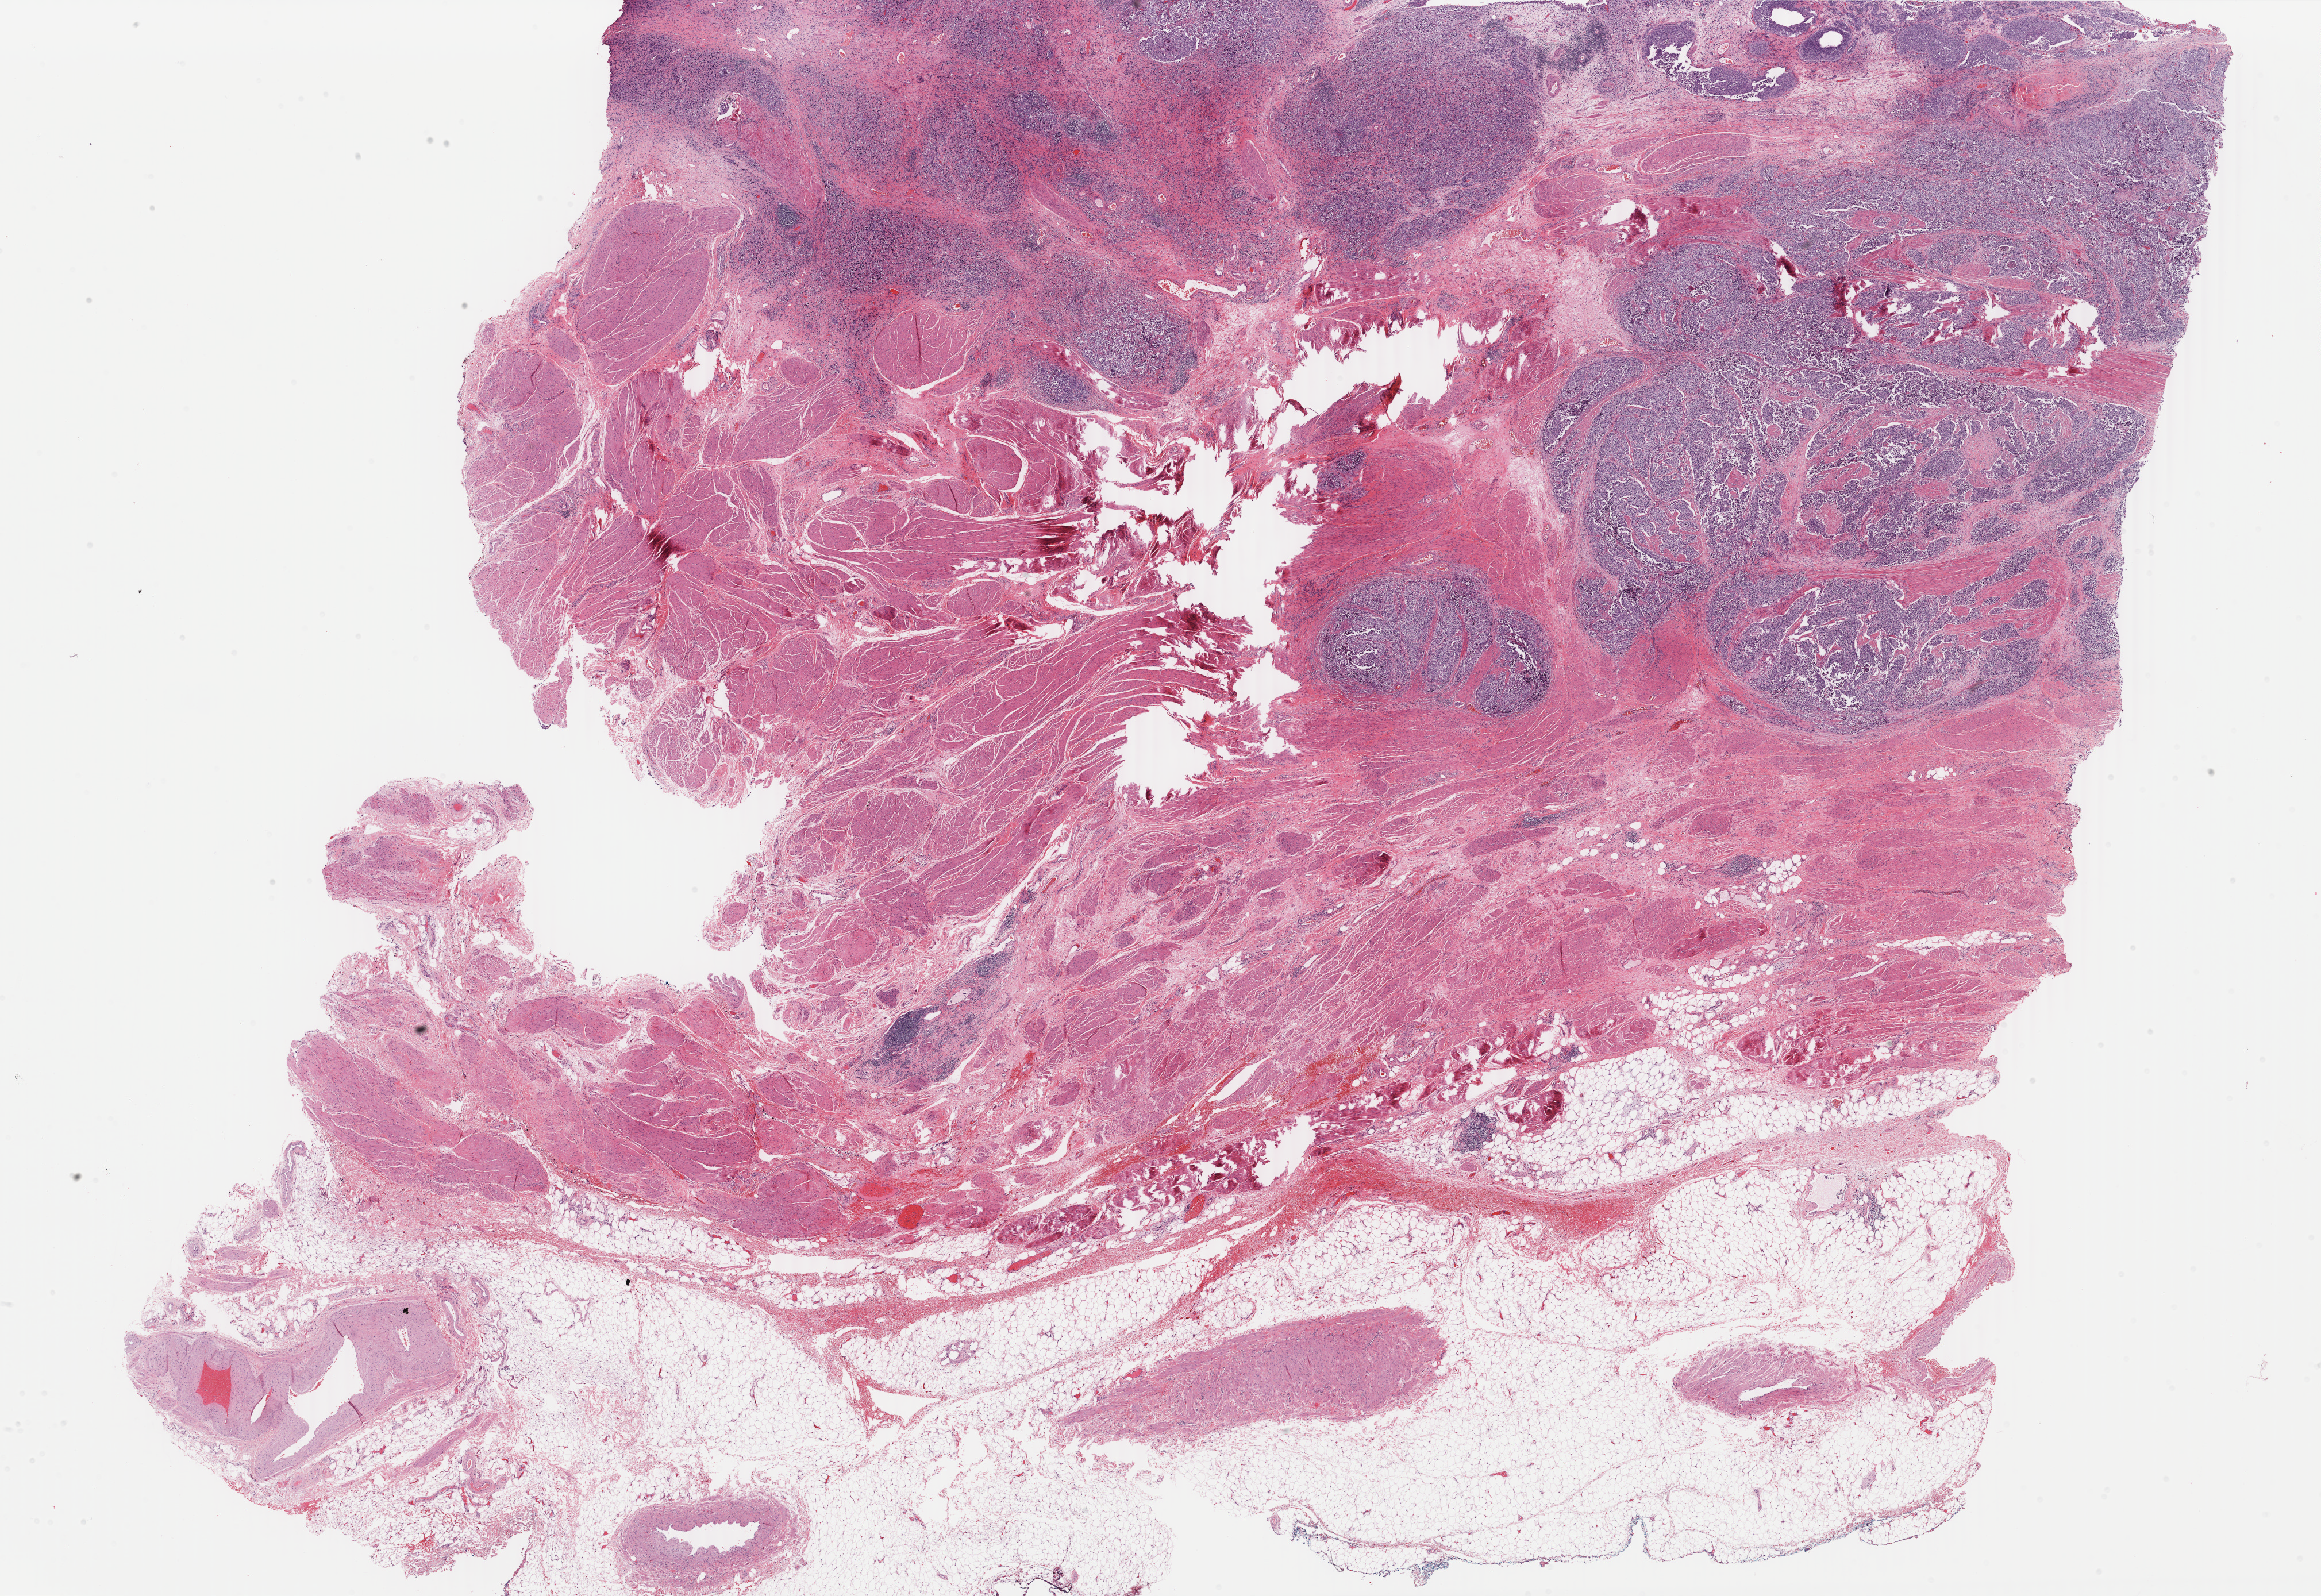
Digitized H&E-stained tissue section (whole slide), shown as a low-resolution overview of the whole scanned area (about 32.1 x 22.1 mm, from a 40x scan). FFPE section. Sample: primary tumour, bladder. Male patient; age at initial diagnosis 59 years. Histologic grade: high grade.
Histologic diagnosis: Transitional cell carcinoma (lateral wall of bladder). AJCC pathologic stage: IV (7th edition). Lymph nodes positive (case pathology): 3 of 16 examined.